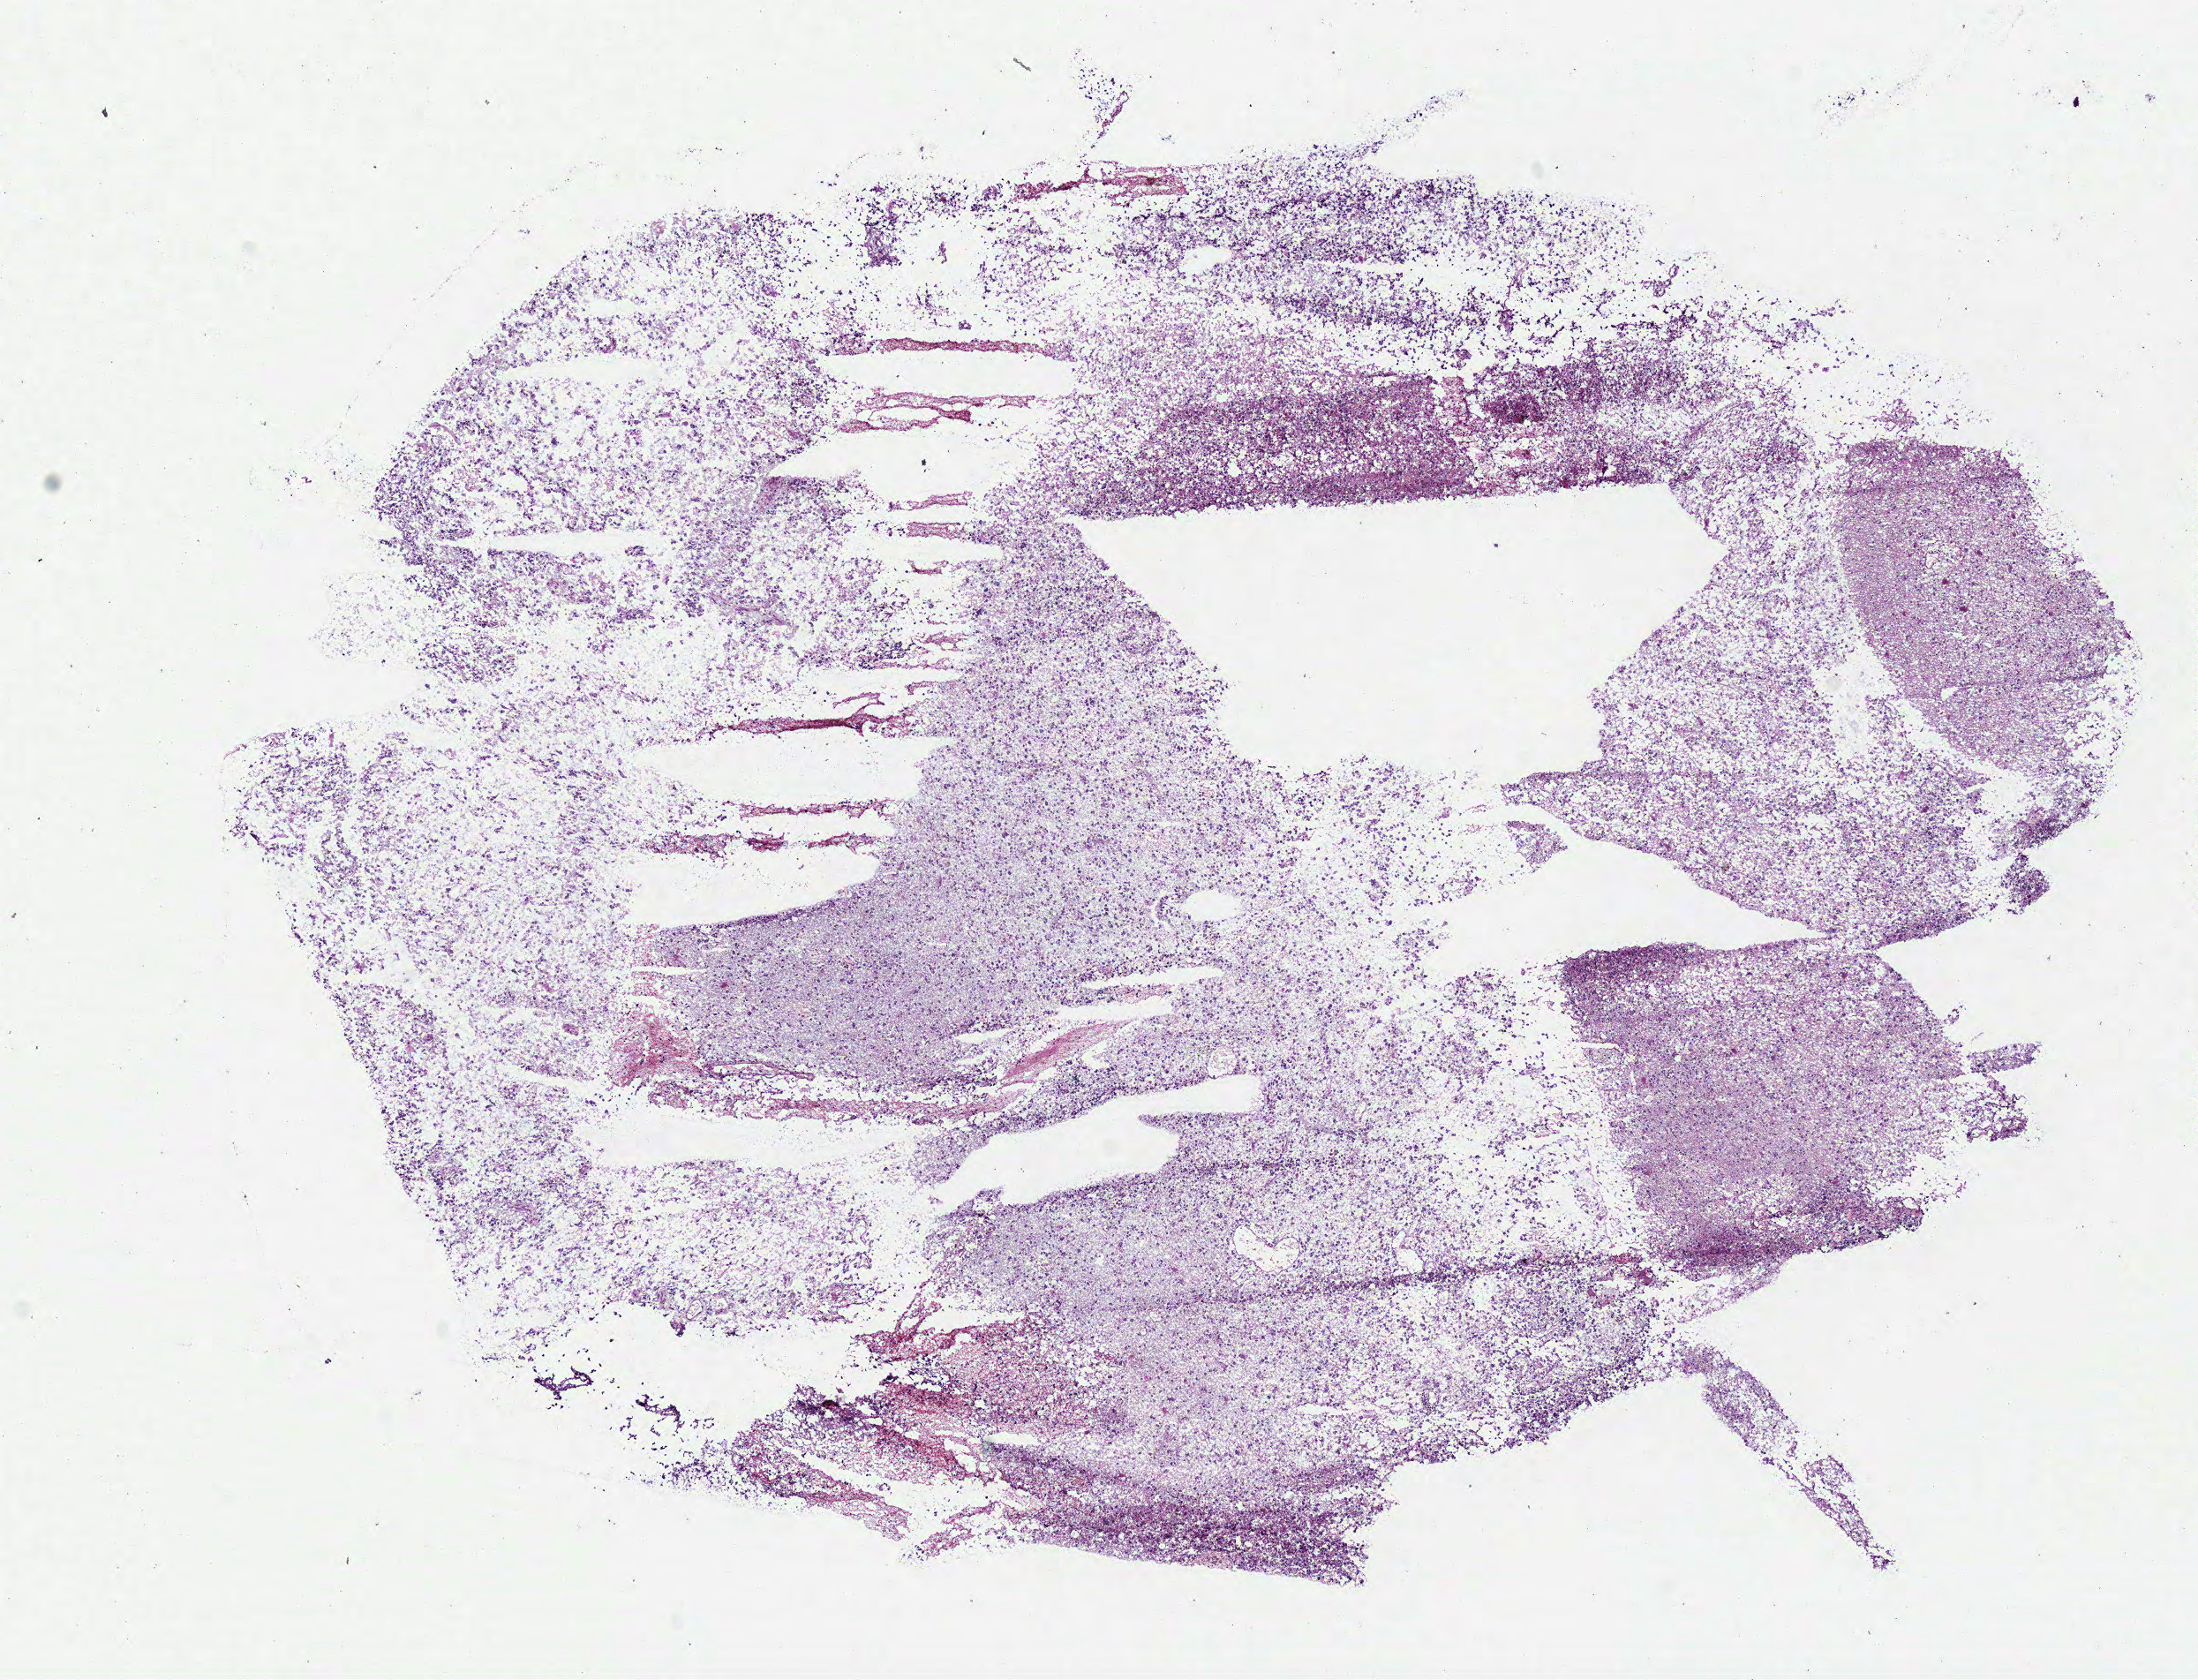
Whole-slide histology image, H&E-stained, shown as a low-resolution overview of the whole scanned area (about 9.8 x 7.5 mm, slide scanned at 40x); frozen section from the bottom of the tissue portion; primary tumour sample from the brain. Female, age 35 years at initial diagnosis. Histologic grade: G3 (poorly differentiated). Pathologist review of this section (percent, as recorded): tumour cells 100%, tumour nuclei 75%, normal cells 0%, stromal cells 0%, necrosis 0%.
- laterality: right
- histologic diagnosis: Astrocytoma, anaplastic (cerebrum)